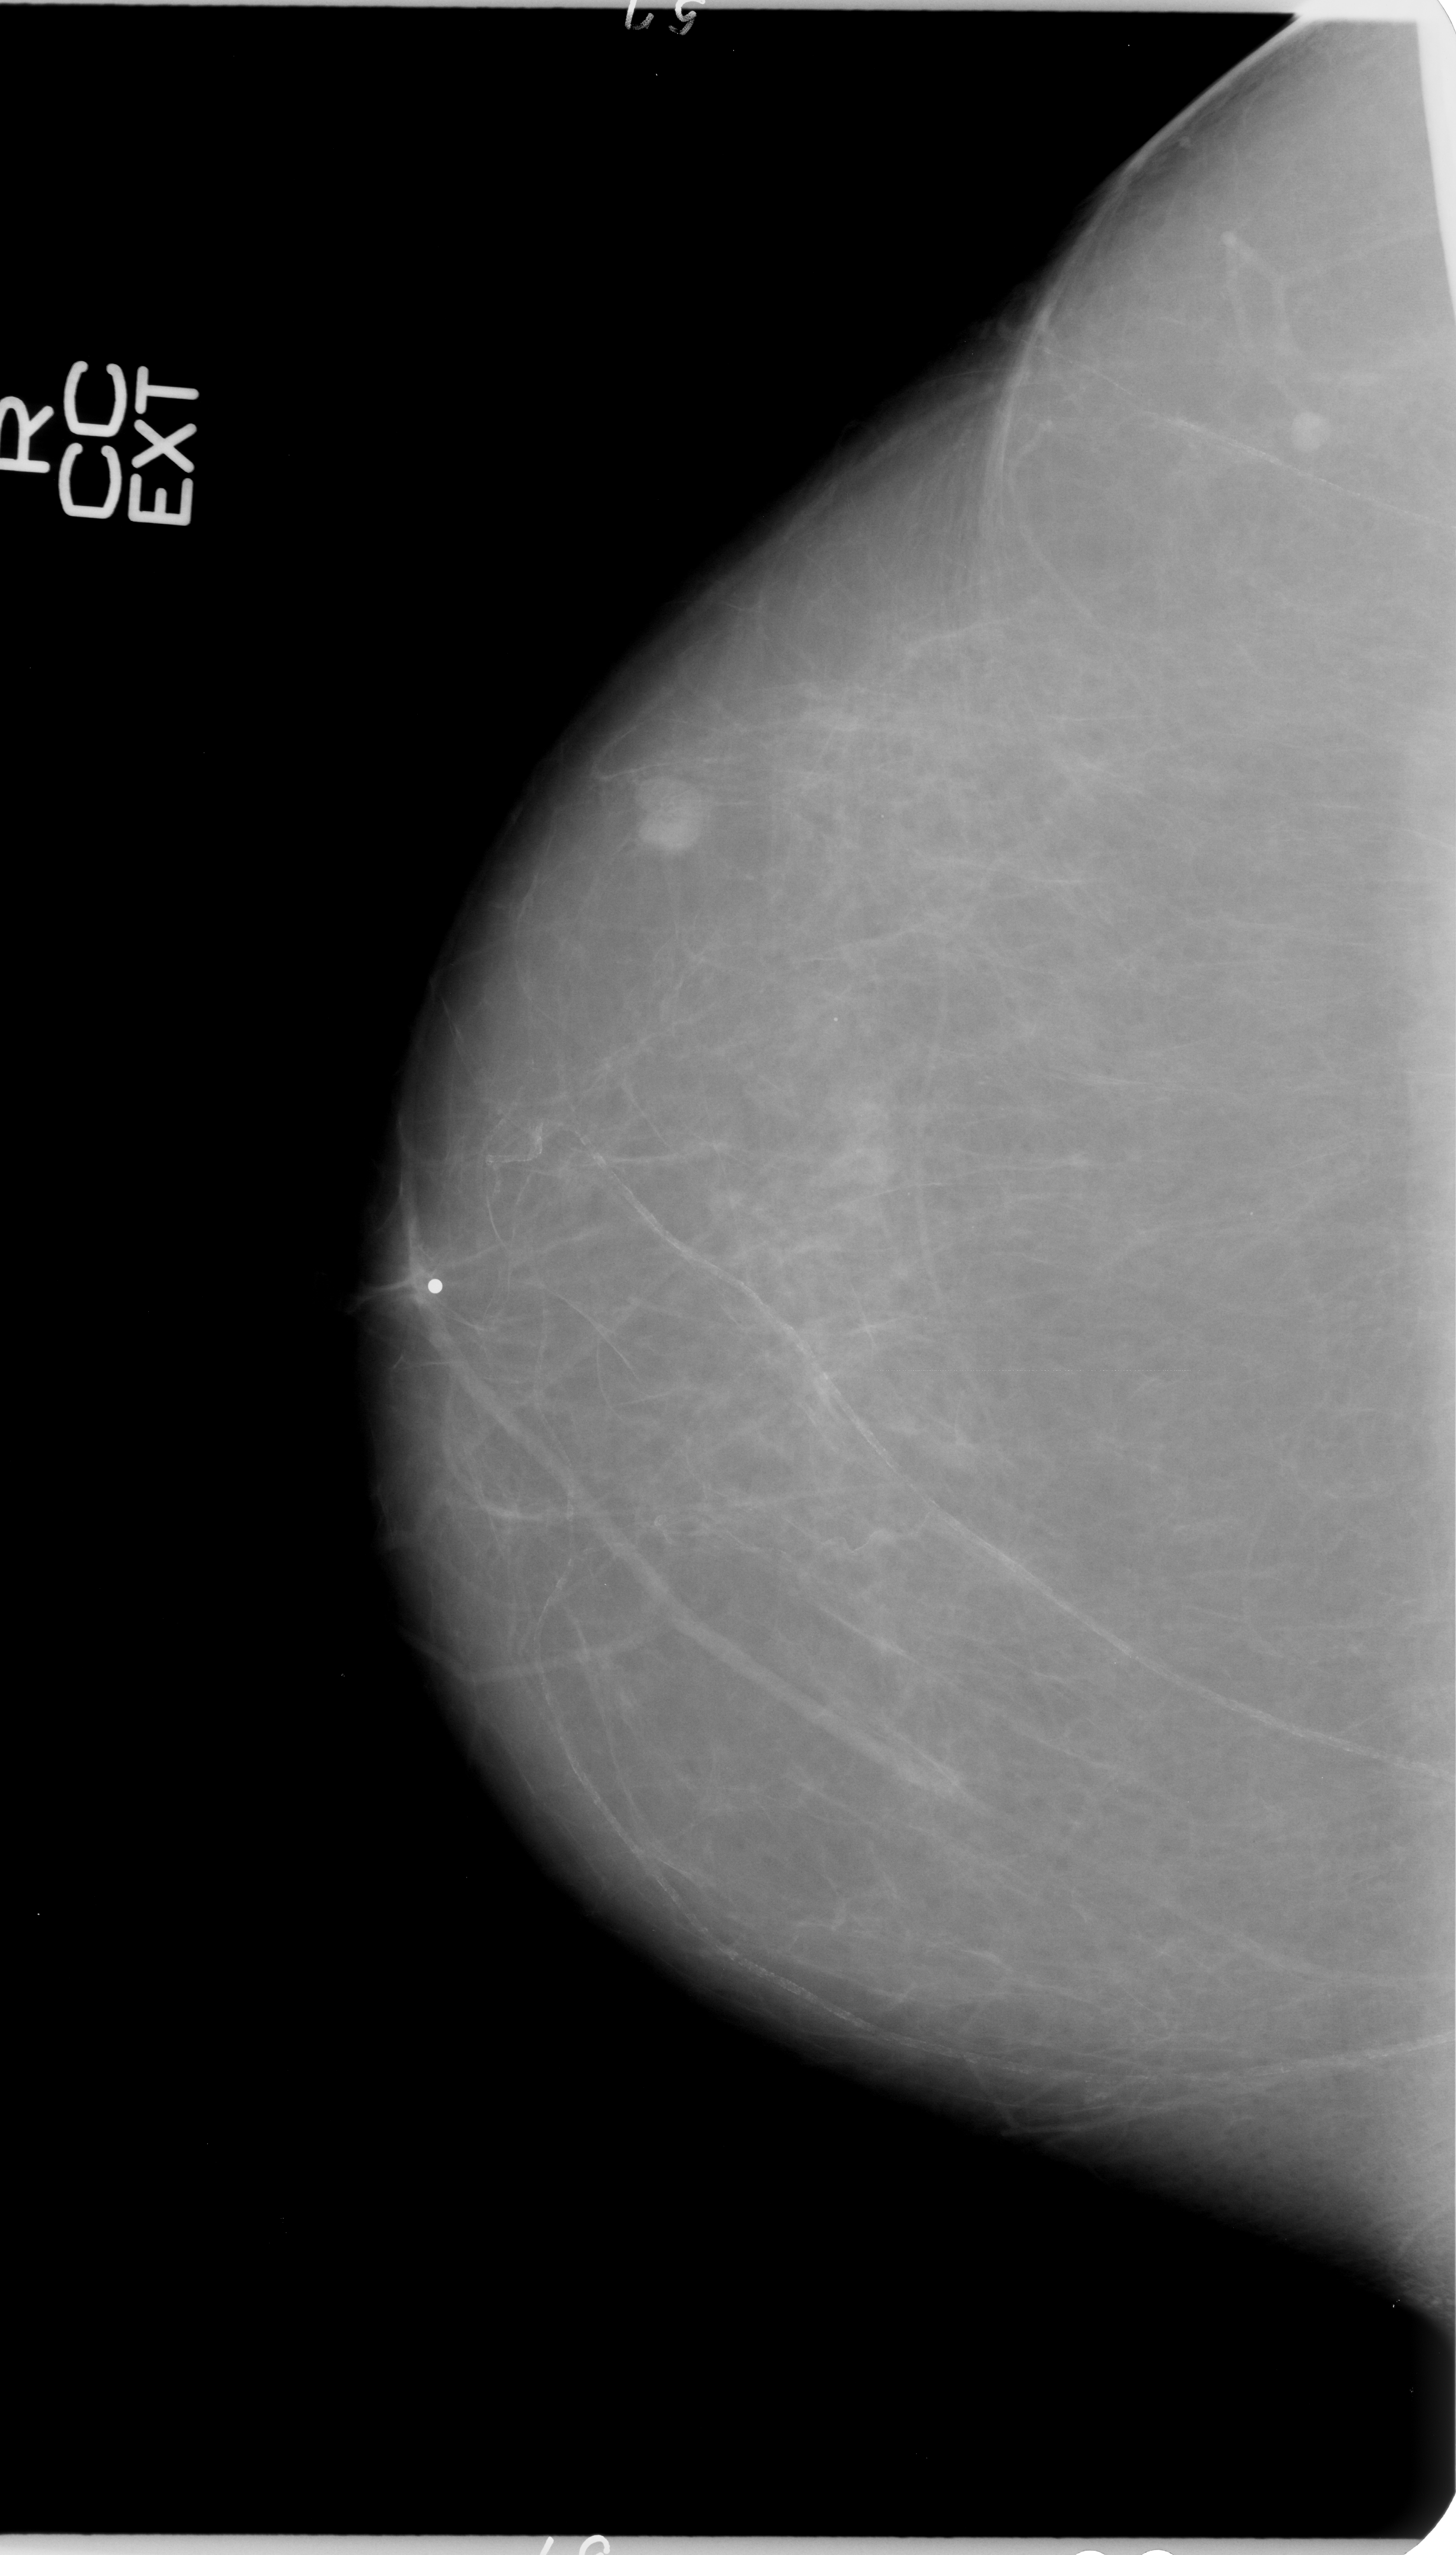
Digitized screen-film mammogram; right breast; CC view; 1456 × 2555 image matrix.
Expert-marked regions of interest on this film, with their recorded descriptors:
- mass, shape irregular, margins ill defined; BI-RADS assessment category 1; subtlety rating 1 on a 1 (subtle) to 5 (obvious) scale; pathology (as recorded): malignant: bounding box [x1, y1, x2, y2] px = [372, 1236, 447, 1314]